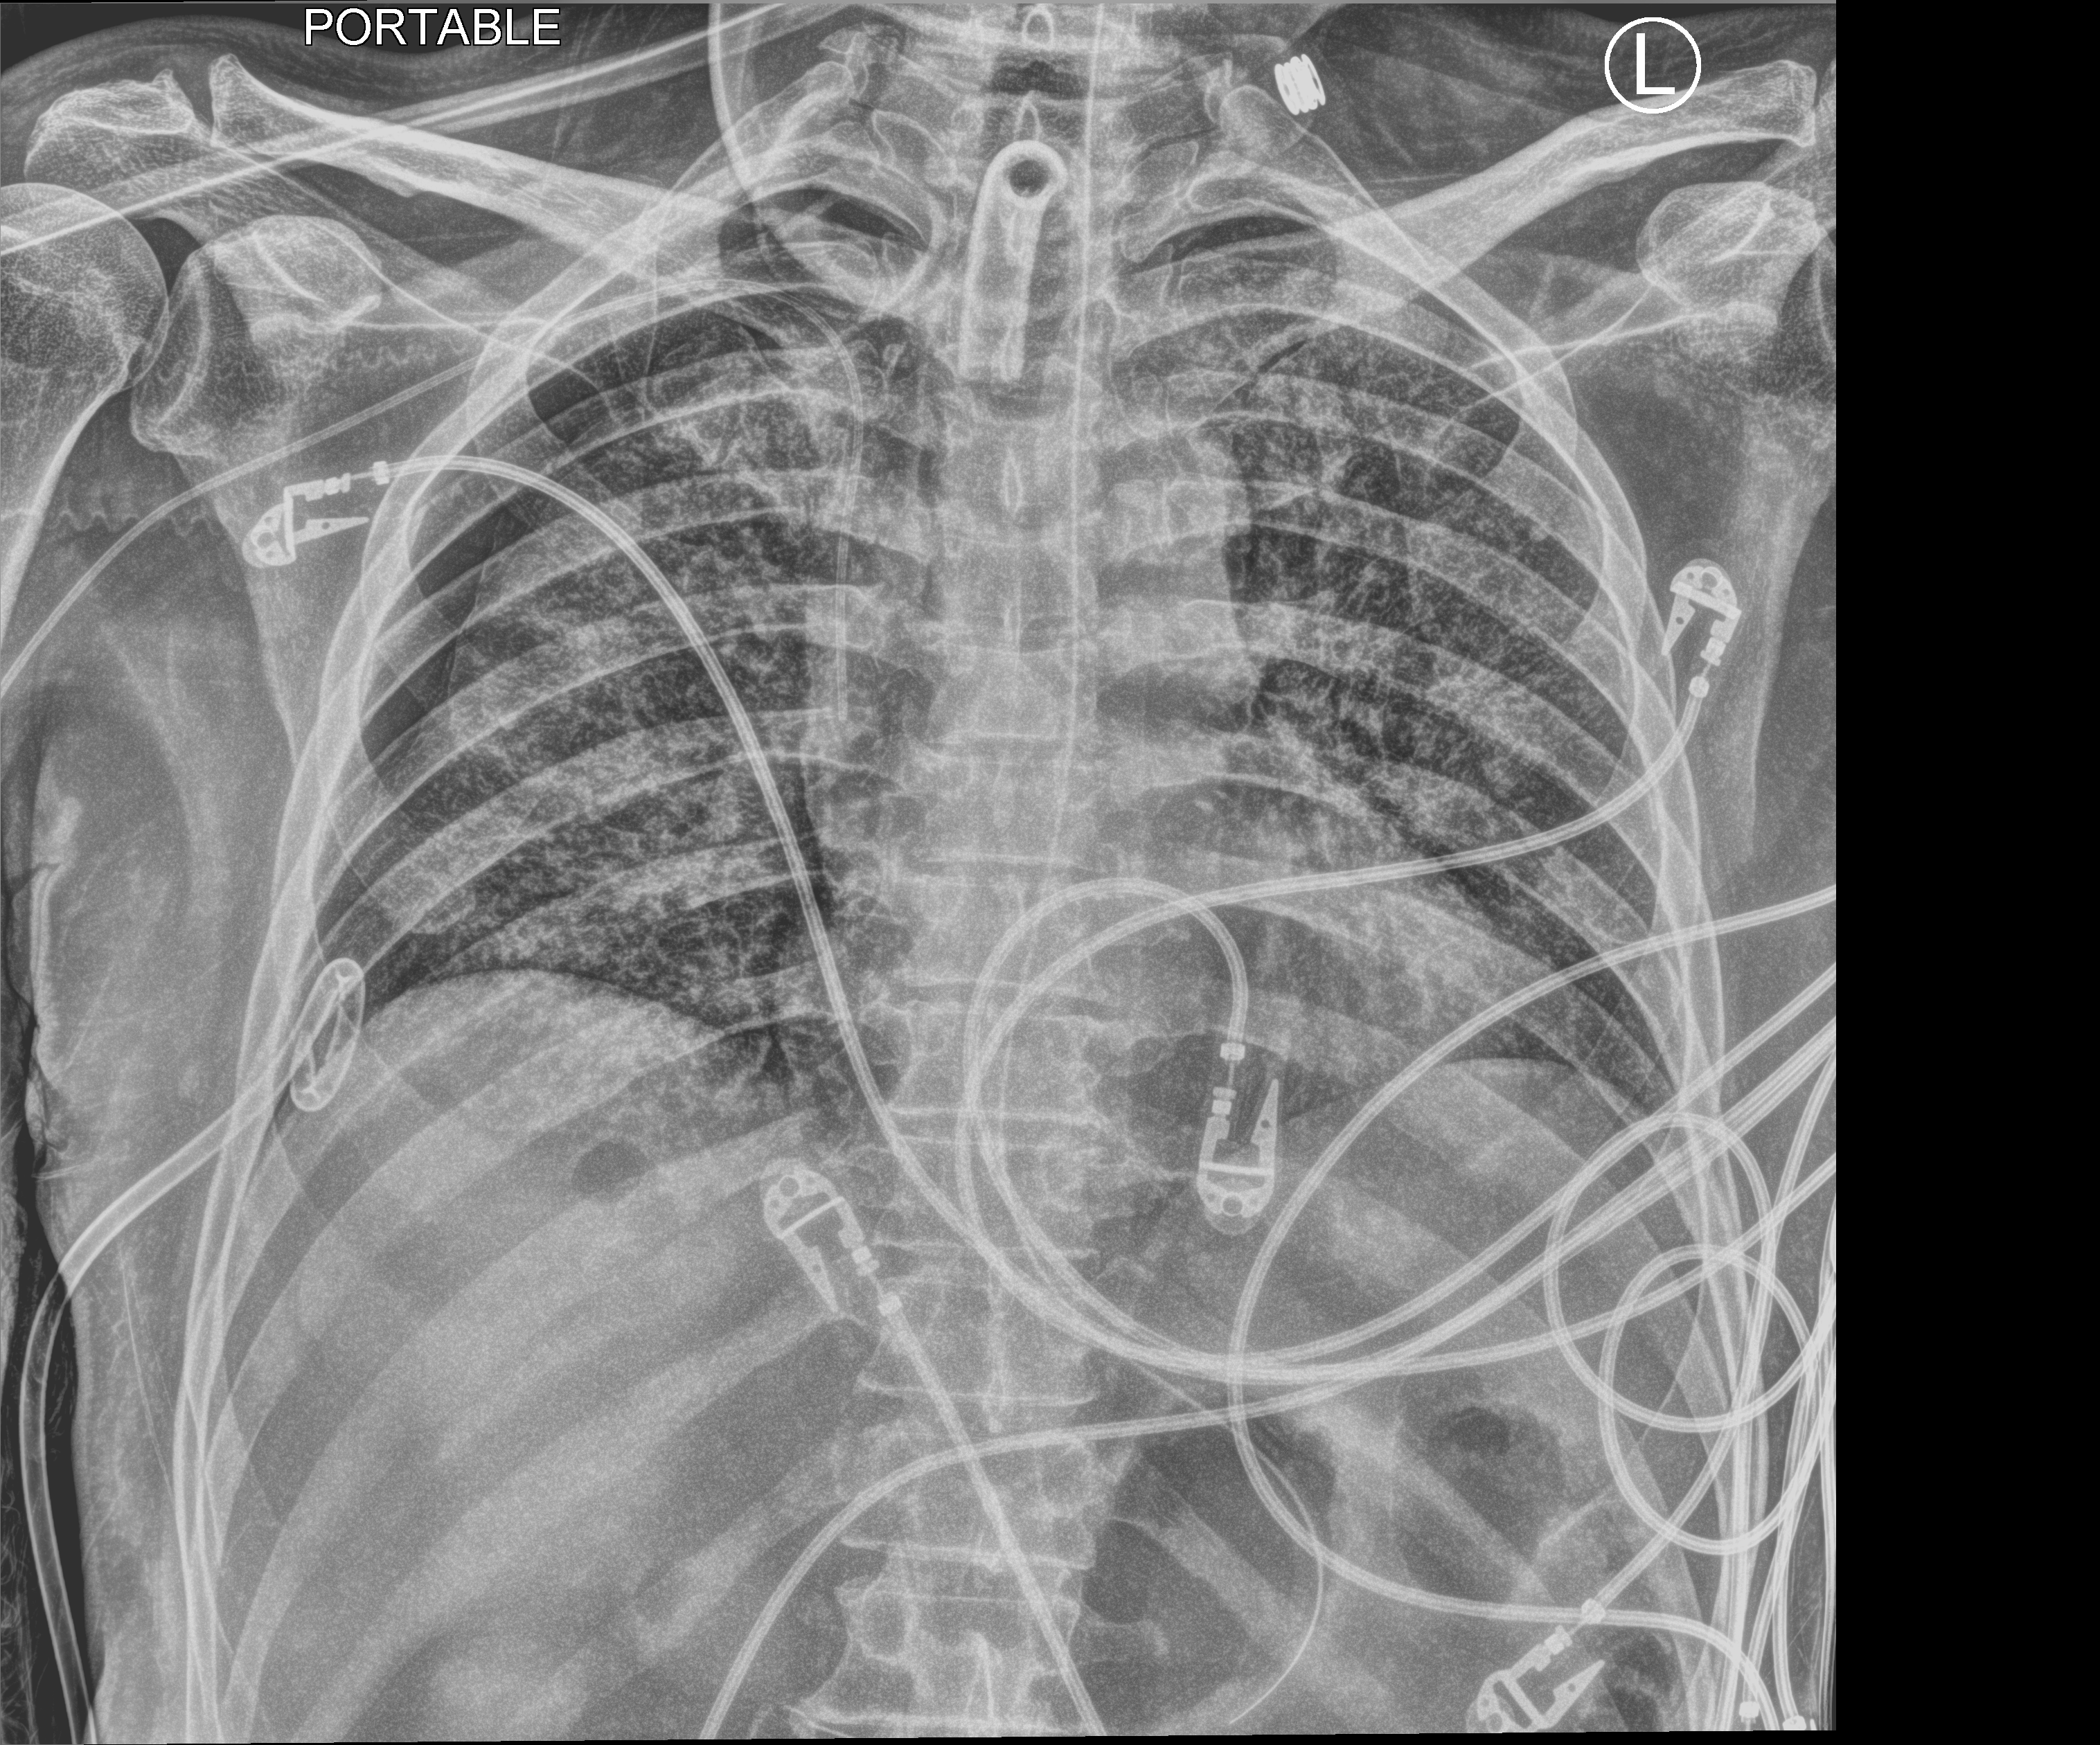
Chest X-ray (portable); anteroposterior (AP) projection. Male patient hospitalised with COVID-19, age 18–59 years.
Admission-level facts for this patient (not findings on this image; timing relative to this image not recorded):
- mechanically ventilated during this hospital stay: yes